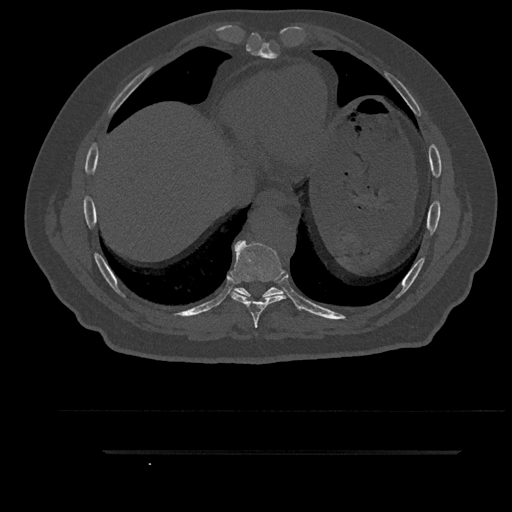
CT including the spine, one axial slice; bone window (W 1800 / L 400 HU); 0.5 mm slice thickness; 512 × 512 image matrix, field of view 432 × 432 mm. Male patient, age 63 years. From the clinical record (not read from this slice): primary cancer: renal; vertebrae with lytic lesions (as recorded): T8.
Structures marked on this image (semi-automatically segmented with operator editing):
- T8 vertebra: bounding box [x1, y1, x2, y2] px = [230, 240, 286, 328]
- T9 vertebra: [233, 287, 283, 297]